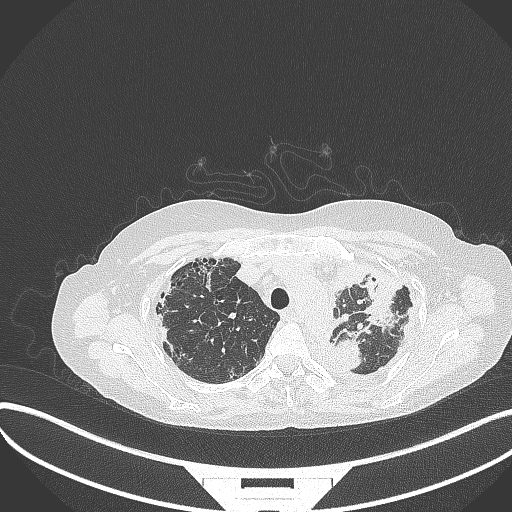
Chest CT, one axial slice; position 268 of 373 along the scan axis; reconstruction kernel B70f; 120 kVp; lung window (W 1500 / L -600 HU); 512 × 512 image matrix, field of view 400 × 400 mm. Patient: female, 56 years. Case-level facts recorded for this patient, not image findings: clinical TNM (as recorded): T1 N0 M0.
Structures marked on this image (rectangle marked by the reading radiologist):
- lung tumour (recorded histology: adenocarcinoma): bounding box <329,328,365,374> (left, top, right, bottom; pixels)
- lung tumour (recorded histology: adenocarcinoma): <358,261,405,335>